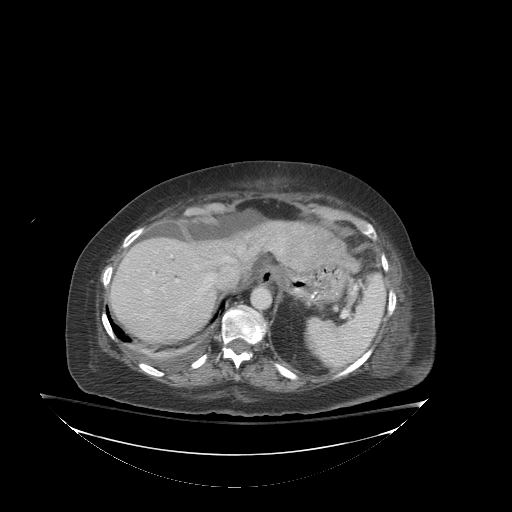
Contrast-enhanced abdominal CT (liver protocol), one axial slice; position 65 of 81 along the scan axis; reconstruction kernel STANDARD; 140 kVp; soft-tissue window (W 400 / L 40 HU); 2.5 mm slice thickness; 512 × 512 image matrix. From the clinical record (not read from this slice): diagnosis: hepatocellular carcinoma (patient treated with transarterial chemoembolisation; whether this scan precedes or follows treatment is not stated here); TNM stage (as recorded): Stage-I; Child-Pugh class: B; tumour differentiation: well-moderately differentiated.
Outlined on this slice (semi-automatic segmentation, software-assisted and operator-edited):
- liver parenchyma outside the tumour (the mass and vessels are separate outlines, so this box may not span the whole liver): bounding box [x1, y1, x2, y2] px = [110, 220, 298, 344]
- liver vessels: [147, 277, 212, 292]